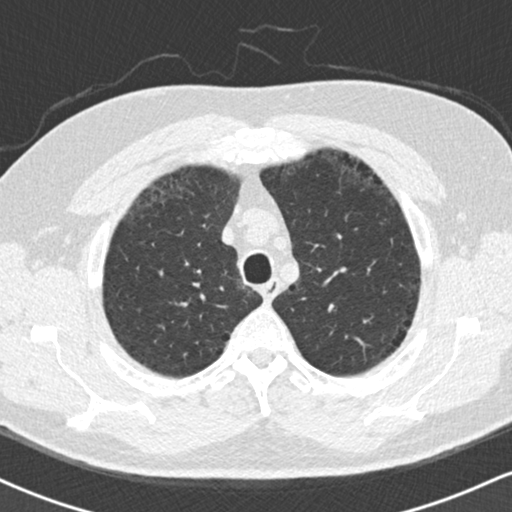
Low-dose screening chest CT, axial slice. Second screening round (one year after baseline). Lung window (W 1500 / L -600 HU). 2 mm slice thickness. Slice 35 of 169 in the series. 512 × 512 image matrix. Male participant, aged 59 years at enrolment. Current smoker at enrolment.
Expert reader's lesion annotation, bounding box <151,317,201,368> (left, top, right, bottom; pixels). The exam's reader record, not a measurement of the box and not confirmed to be the same lesion: non-calcified nodule or mass ≥4 mm, right upper lobe, 18 × 16 mm, ground glass attenuation, pre-existing on the prior screen: yes. Later outcome: lung cancer diagnosed 60 days after this screen — bronchiolo-alveolar adenocarcinoma, NOS, right lower lobe, stage IA (AJCC 6th edition), 15 mm at pathology.